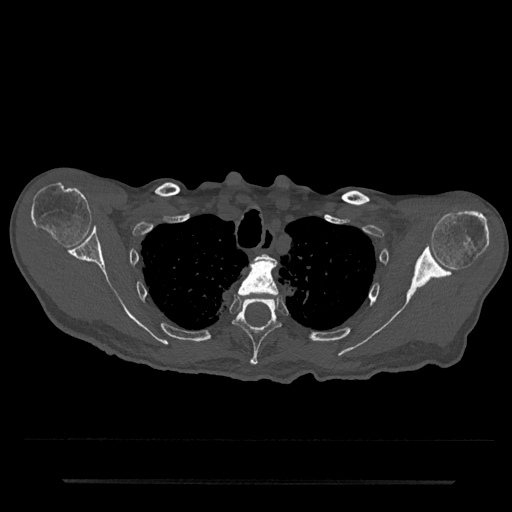
CT including the spine, one axial slice; slice 631 of 797 in the series (ordered by position); reconstruction kernel Br40s/3; 120 kVp; bone window (W 1800 / L 400 HU); 512 × 512 image matrix, field of view 427 × 427 mm. Male patient, age 74 years. From the clinical record (not read from this slice): primary cancer: prostate.
Structures marked on this image (semi-automatic segmentation, software-assisted and operator-edited):
- T2 vertebra: box from (x=257, y=253) to (x=273, y=261) px
- T3 vertebra: (x=238, y=258)–(x=279, y=295)
- T4 vertebra: (x=233, y=299)–(x=281, y=365)